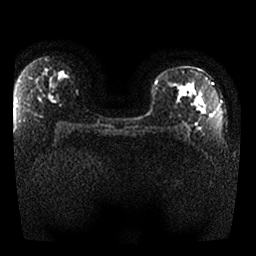
Breast MRI, one axial slice; position 17 of 25 along the scan axis; diffusion-weighted series; image 2 of 4 stored at this slice position (different b-values; order by instance number); 1.5 T; 4 mm slice thickness; 256 × 256 image matrix, field of view 330 × 330 mm. Female patient.
Outlined on this slice (expert manual segmentation):
- tumour on diffusion-weighted imaging: box from (x=179, y=85) to (x=206, y=114) px